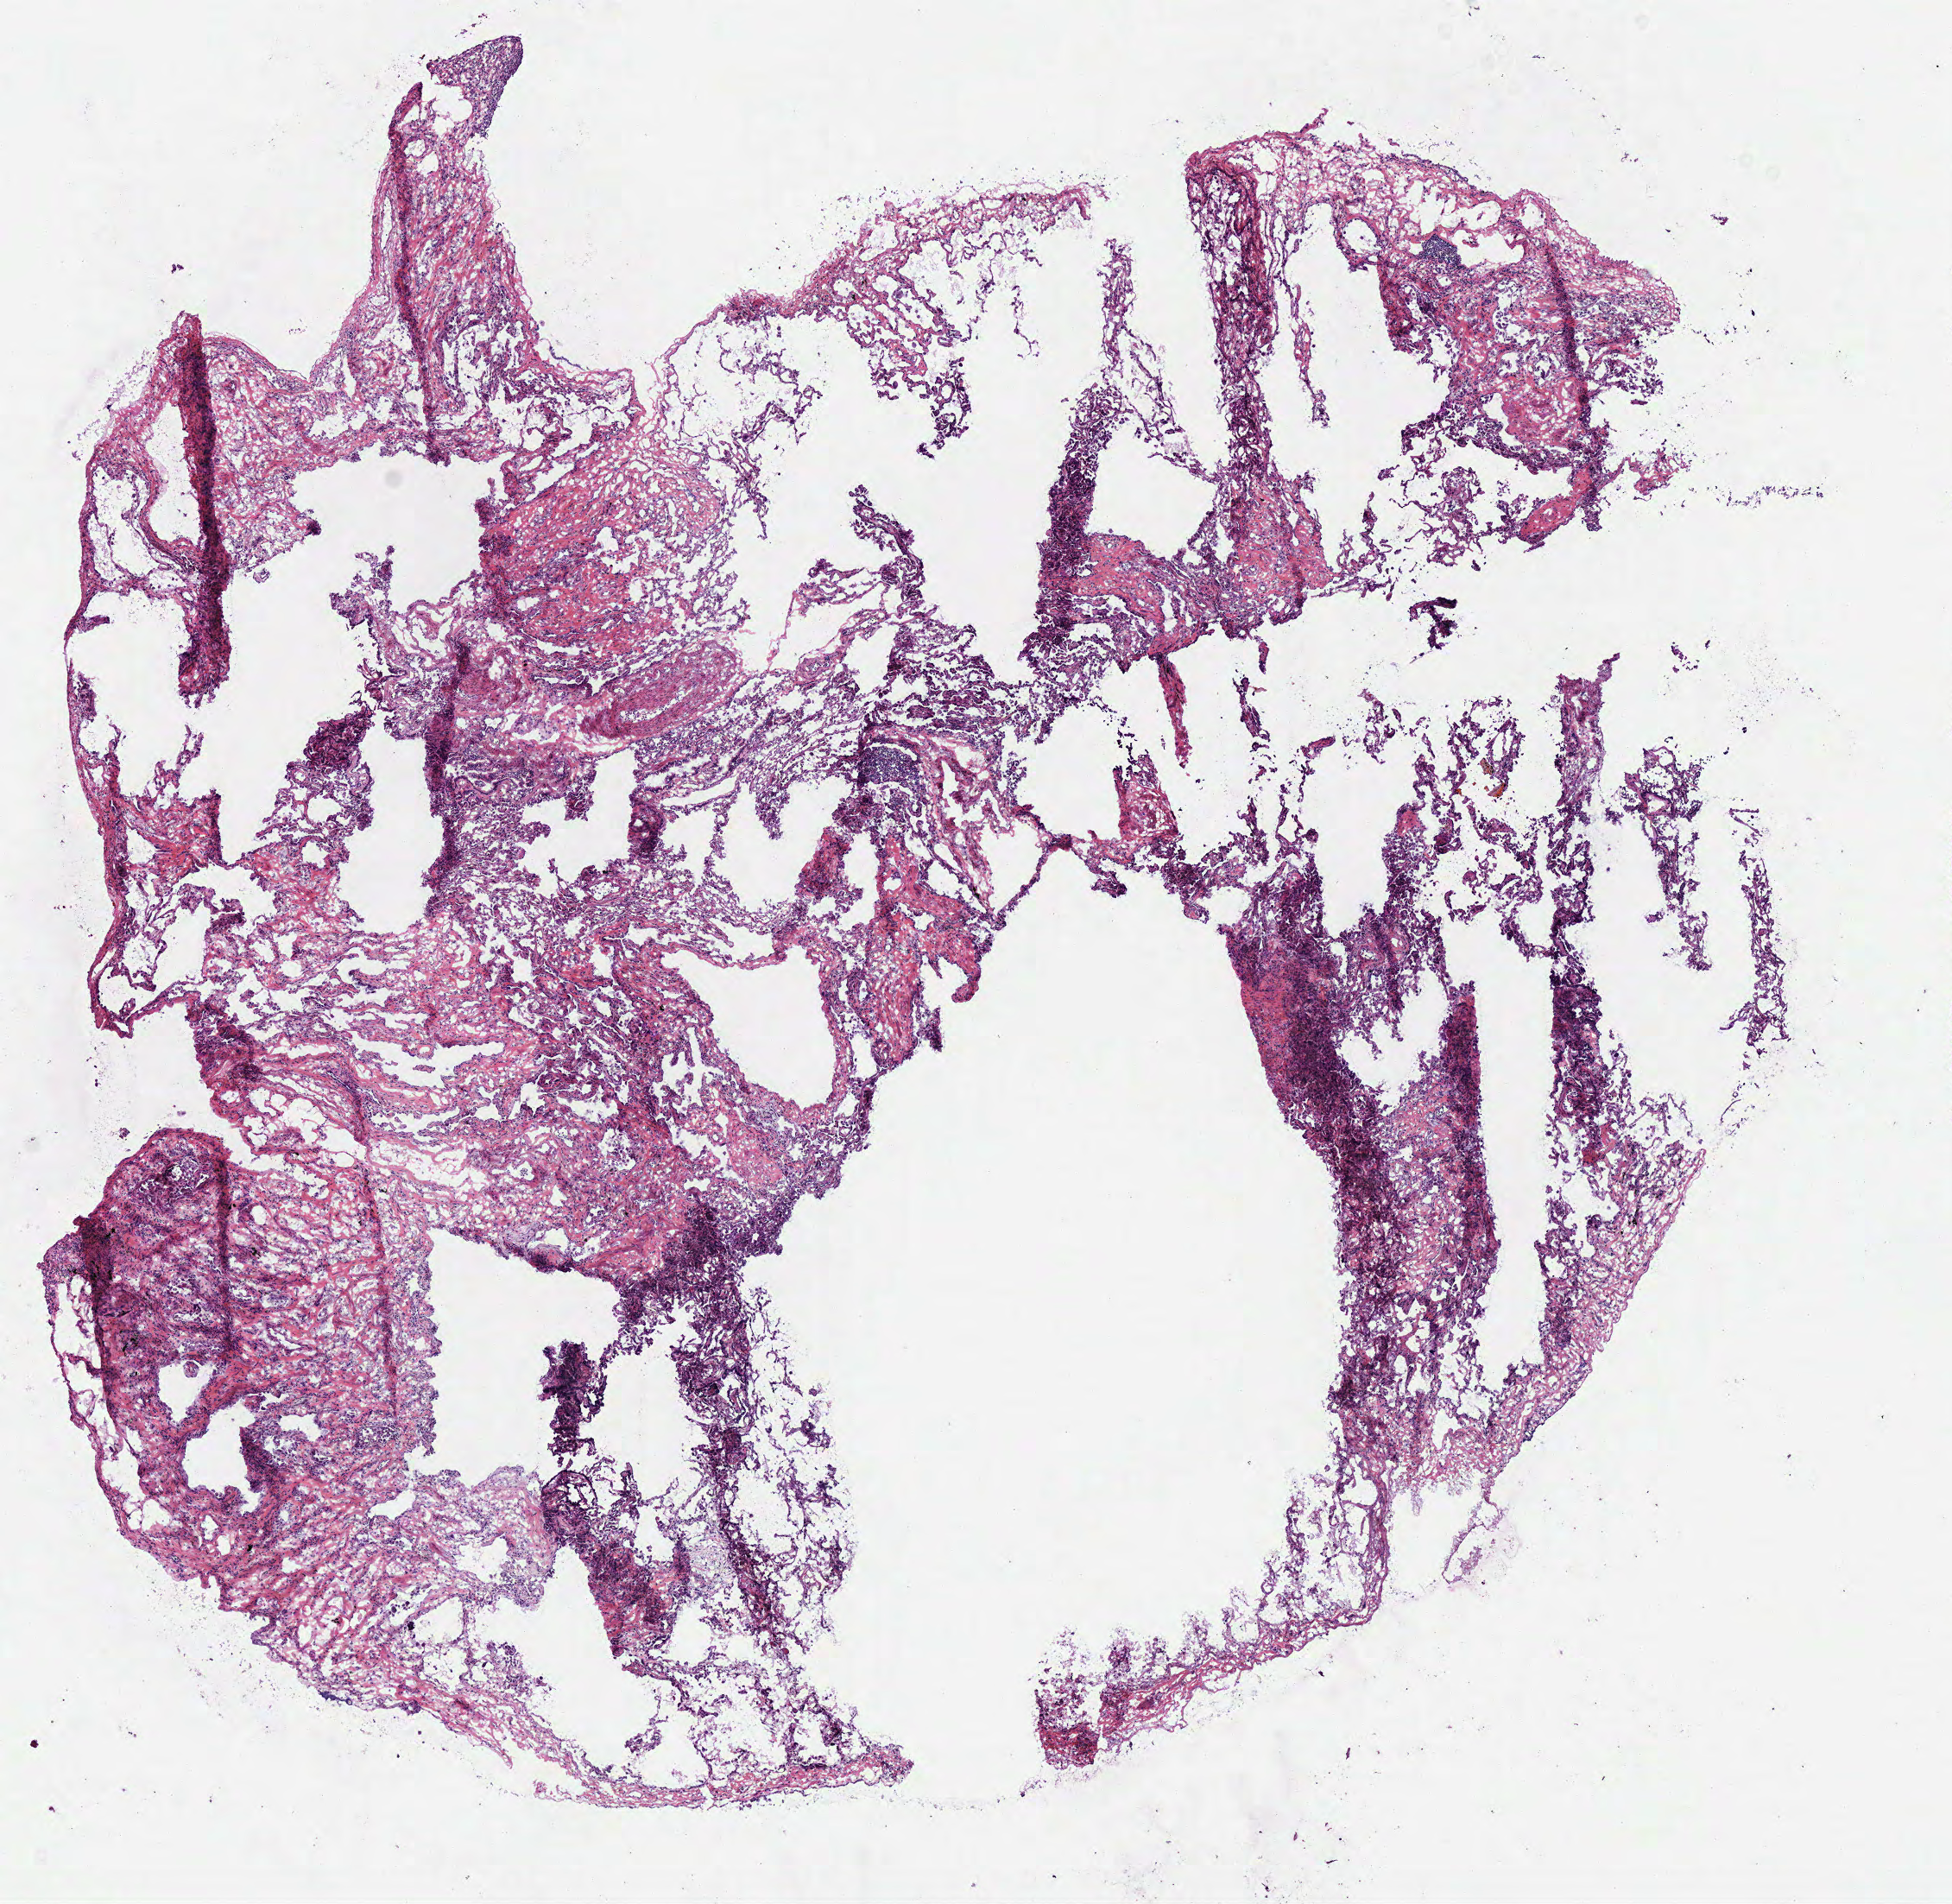
Whole-slide histology image, Hematoxylin and eosin (H&E) stained — low-resolution overview of the scanned area, about 8.9 x 8.7 mm (acquisition: 40x scan). Frozen section from the top of the tissue portion. Solid tissue normal (non-tumour tissue) sample from the lung. Male patient; age at initial diagnosis 70 years.
- this section: solid tissue normal sample (biorepository sample class)
- patient diagnosis: Mucinous adenocarcinoma